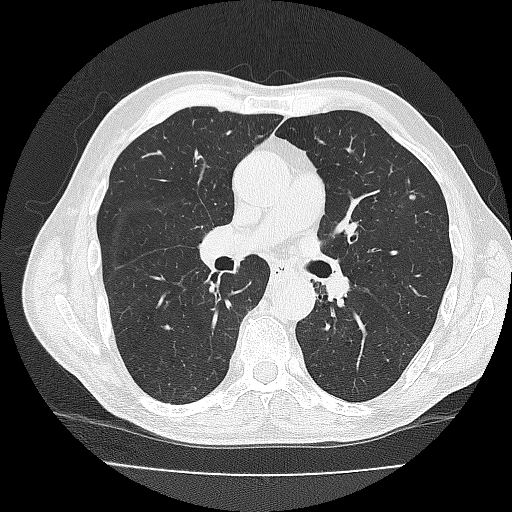
Chest CT (low-dose screening protocol), one axial image, second screening round (one year after baseline), lung window (W 1500 / L -600 HU), 120 kVp, slice 95 of 206 in the series. Male, age 71 years at enrolment. Current smoker at enrolment.
Lesion marked by an expert reader, bounding box [x1, y1, x2, y2] px = [390, 179, 433, 220]. Screening reader's record for this exam: no non-calcified nodule ≥4 mm recorded. Lung cancer was diagnosed 387 days after this screen: adenocarcinoma, NOS, left upper lobe, moderately differentiated (G2), stage IA (AJCC 6th edition), 10 mm at pathology.